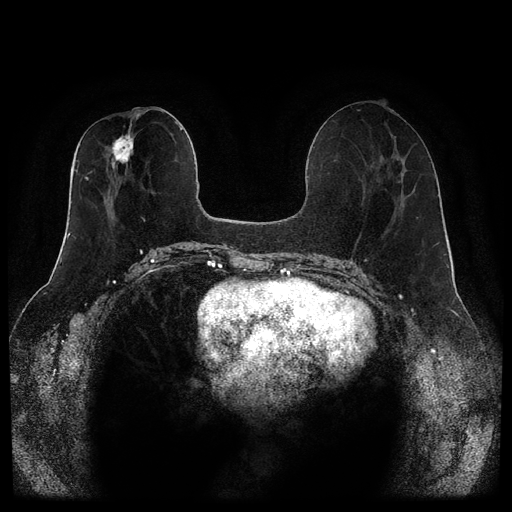
Breast MRI (dynamic contrast-enhanced, multi-phase), one axial slice; position 45 of 116 along the scan axis; dynamic contrast-enhanced series, time point 2 of 5 at this slice position (early post-contrast); 1.5 T; TE 2.6 ms, TR 5.3 ms; 2 mm slice thickness; 512 × 512 image matrix, field of view 350 × 350 mm. Female patient, age 46 years.
Structures marked on this image (semi-automatically segmented with operator editing):
- breast lesion (labelled 'tumour' in the annotation; benign lesions carry a separate 'benign' label): bounding box (x1, y1, x2, y2) in pixels: (111, 120, 134, 167)